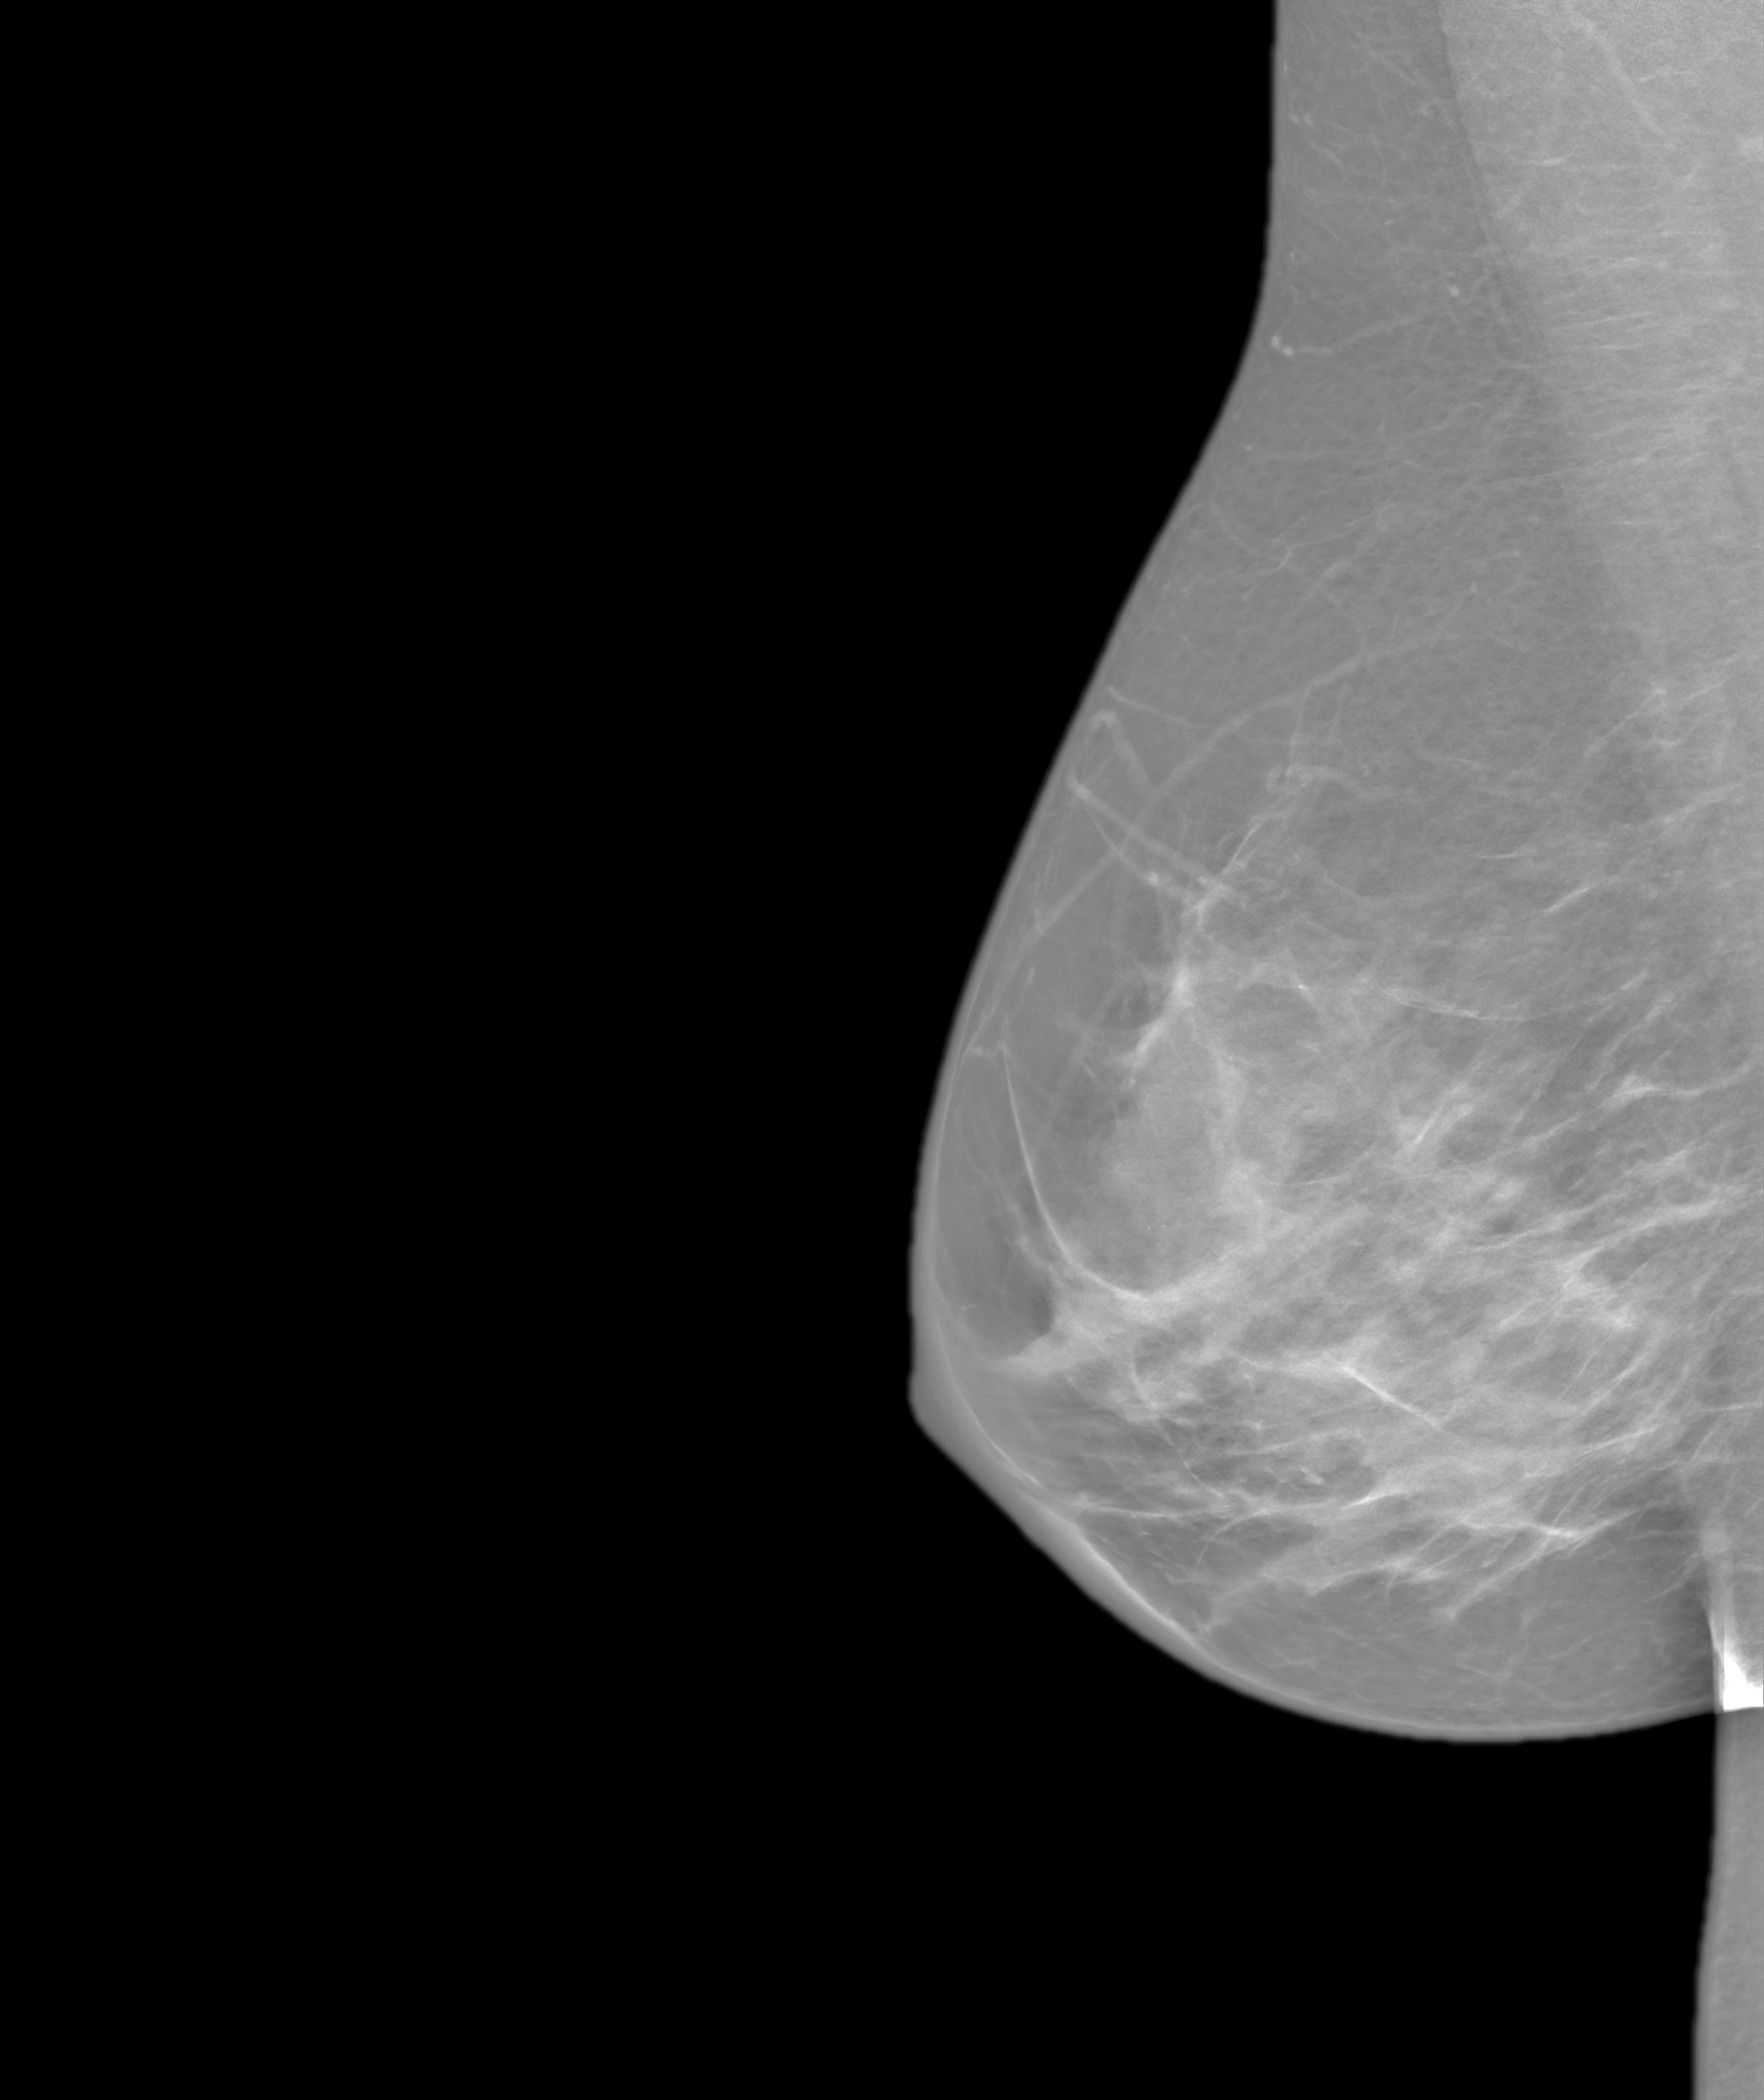
Screening examination. Female patient, age 45 years.
Image type: synthesized 2-D view from tomosynthesis. Breast: right. Projection: mediolateral oblique (MLO) view.